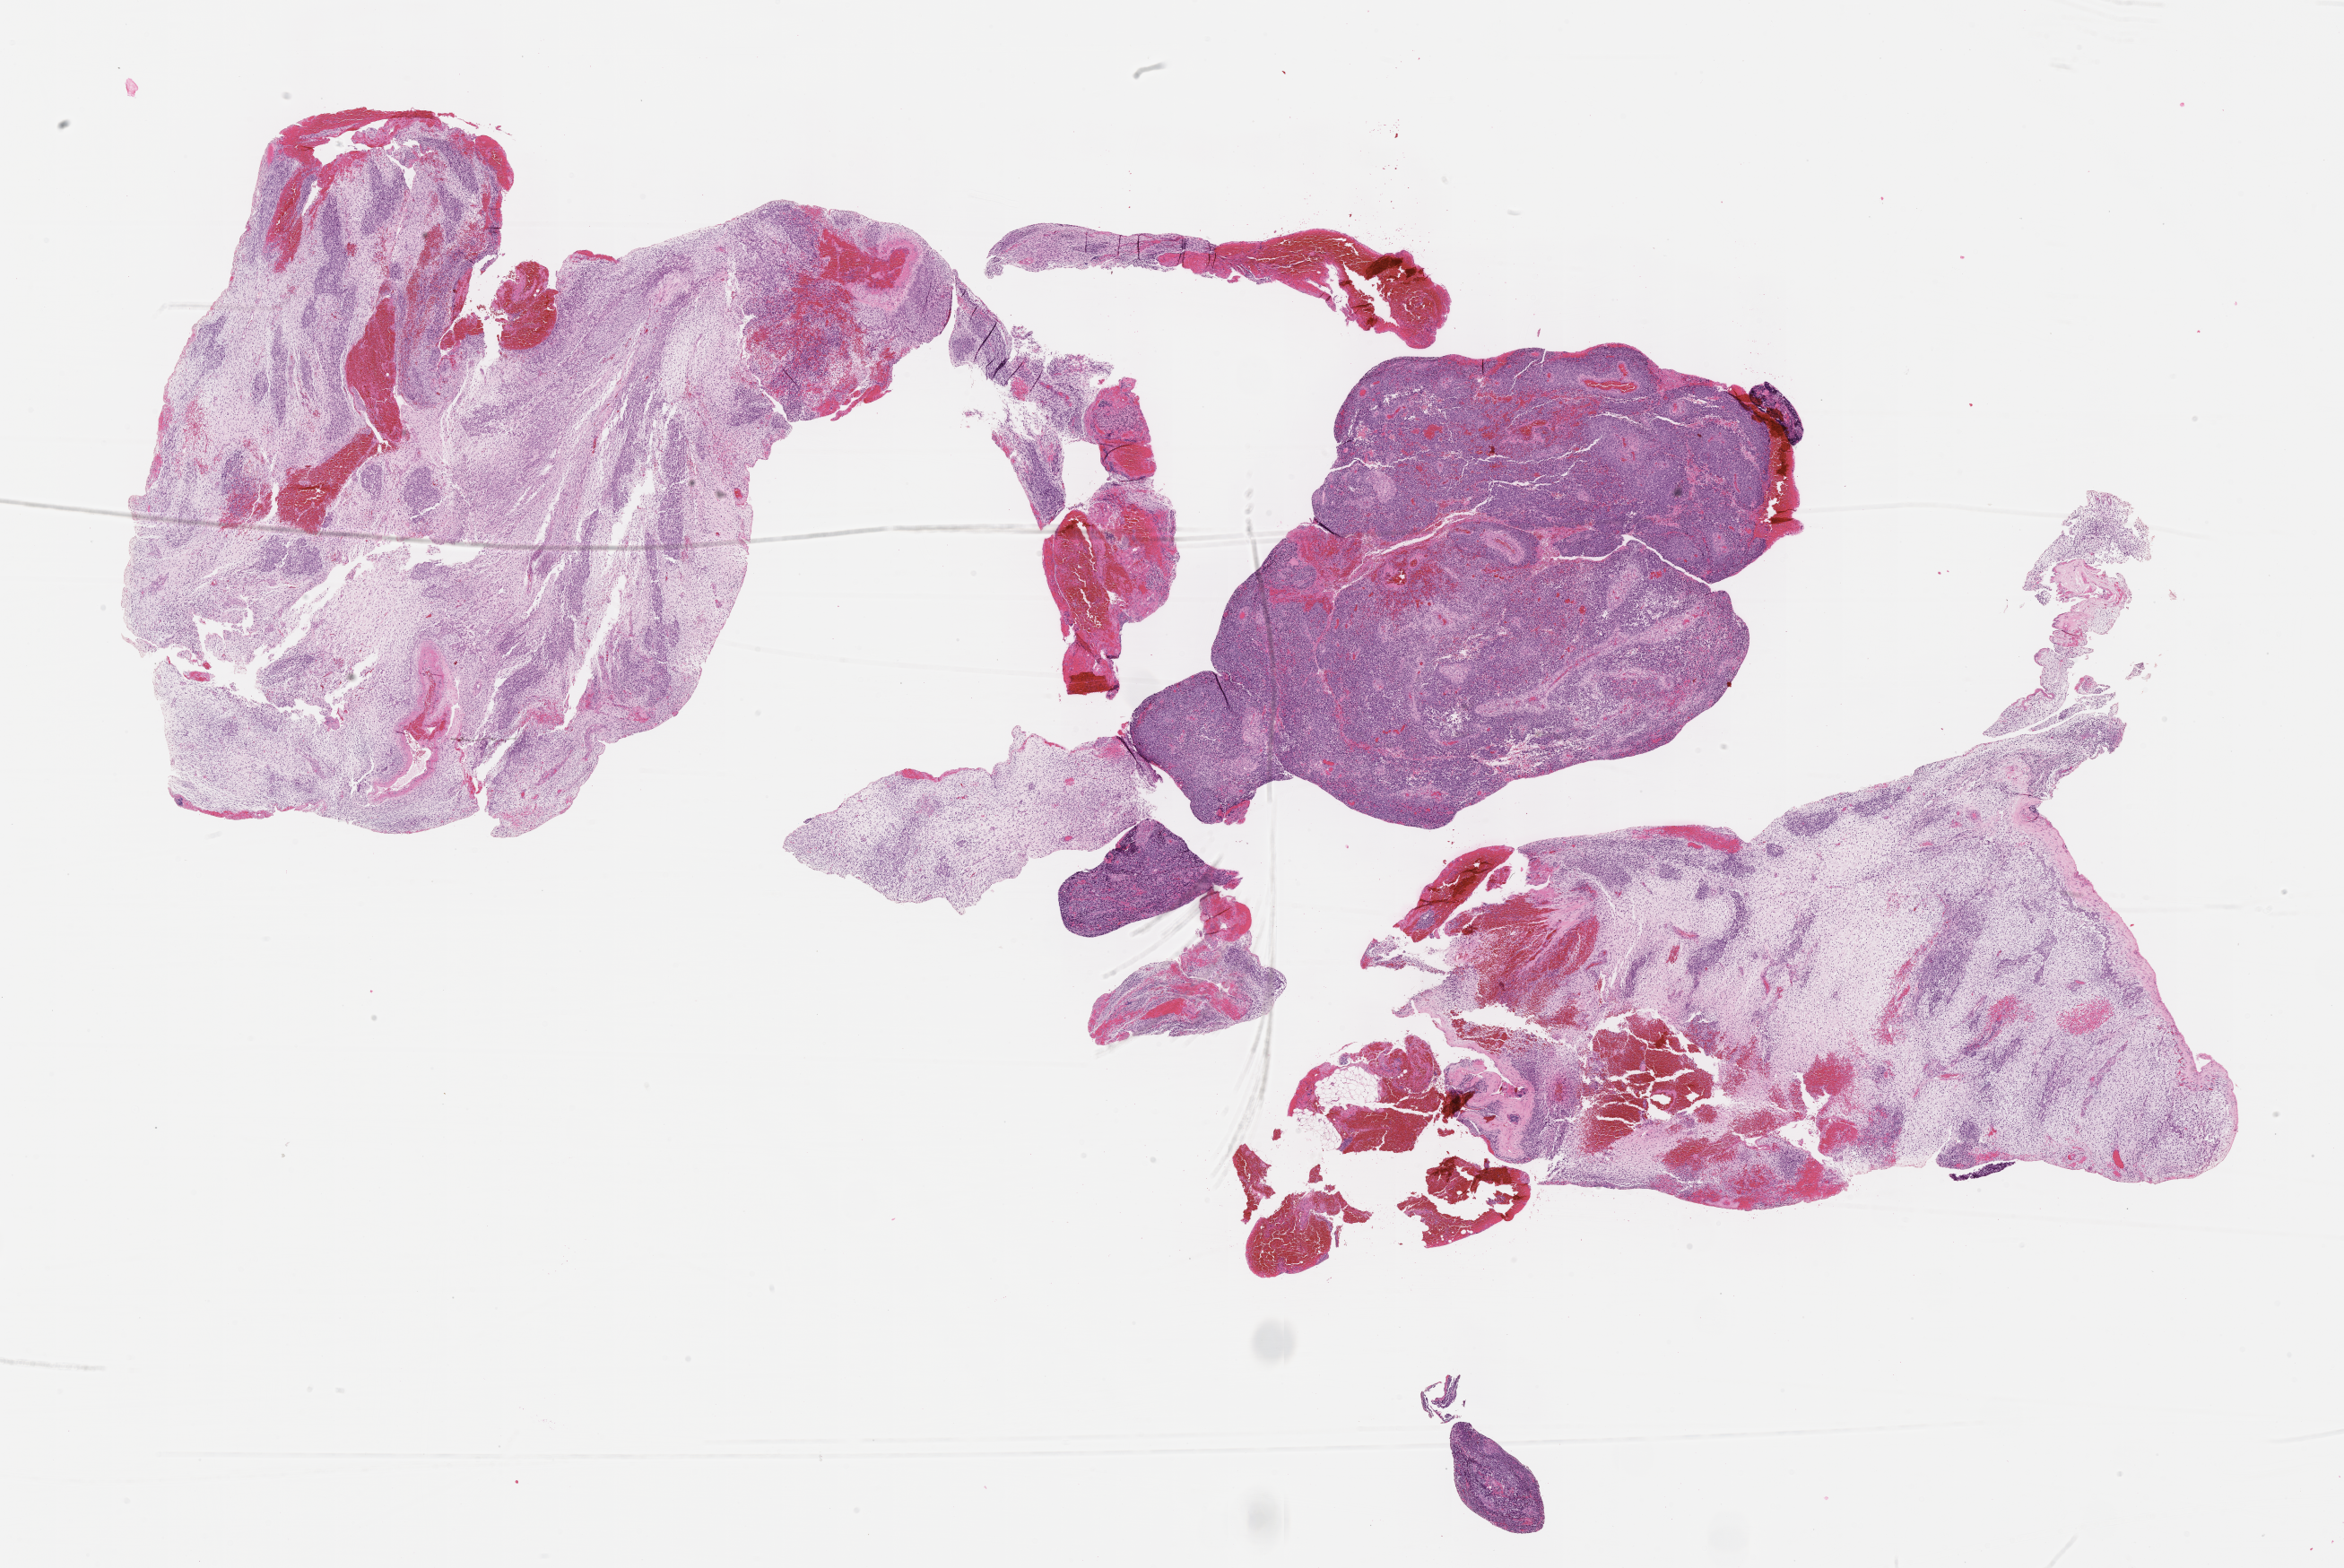
Digitized H&E-stained section of tumor tissue, shown as a low-resolution overview of the whole scanned area (about 21.1 x 14.1 mm), formalin-fixed paraffin-embedded section, sample anatomic site: abdomen. Female patient, age at diagnosis 3.6 years.
Metastatic status at presentation (as recorded): non-metastatic. Primary site (case record): bladder. Diagnosis: rhabdomyosarcoma; histological classification: embryonal rhabdomyosarcoma. Stage (as recorded): 3.